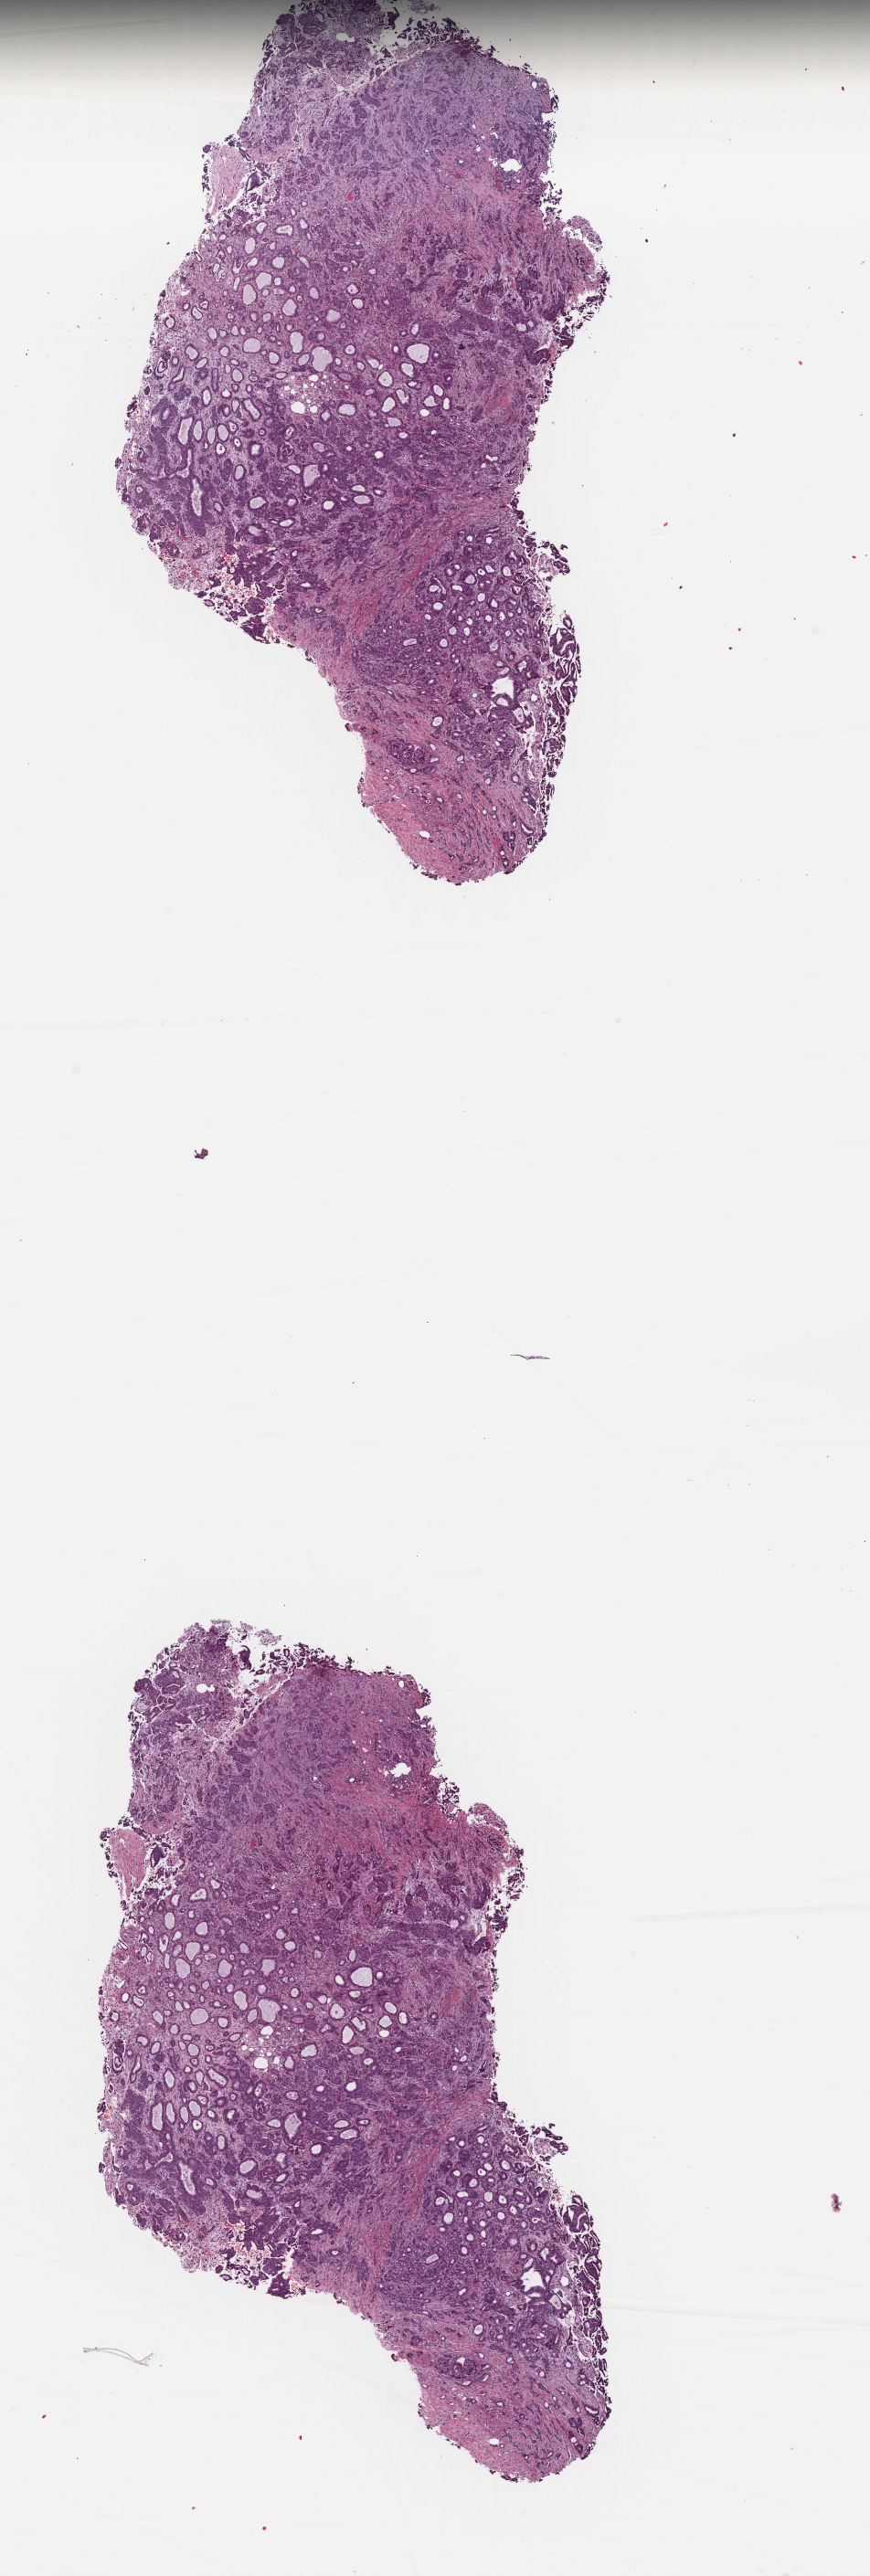
Whole-slide histology image, H&E, a low-resolution overview of the entire scanned area, about 7.5 x 22.2 mm (slide scanned at 40x). Formalin-fixed paraffin-embedded (FFPE) diagnostic section. Sample: primary tumour, breast. Patient: female, age at initial diagnosis 79 years.
AJCC pathologic stage: IIA. Pathologic diagnosis: Infiltrating duct carcinoma, NOS. Lymph nodes positive (case pathology): 0 of 2 examined.